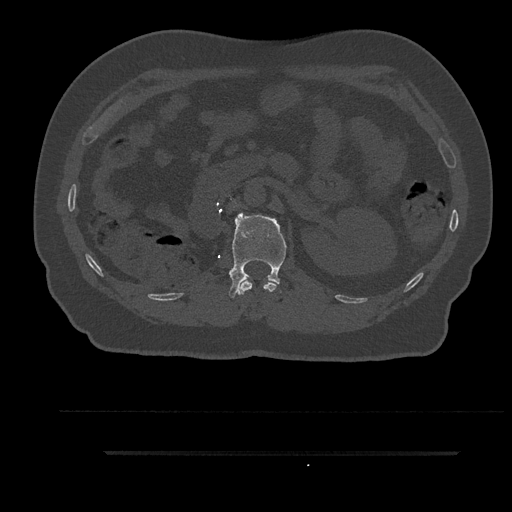
CT including the spine, one axial slice. Position 191 of 797 along the scan axis. Reconstruction kernel Br40s/3. Bone window (W 1800 / L 400 HU). 0.5 mm slice thickness. 512 × 512 image matrix. Patient: male, 63 years. Case-level facts recorded for this patient, not image findings: primary cancer: renal; vertebrae with lytic lesions (as recorded): T8.
Annotated regions visible in this slice (semi-automatically segmented with operator editing):
- L1 vertebra: bounding box (x1, y1, x2, y2) in pixels: (229, 213, 287, 298)
- T12 vertebra: (240, 280, 278, 295)